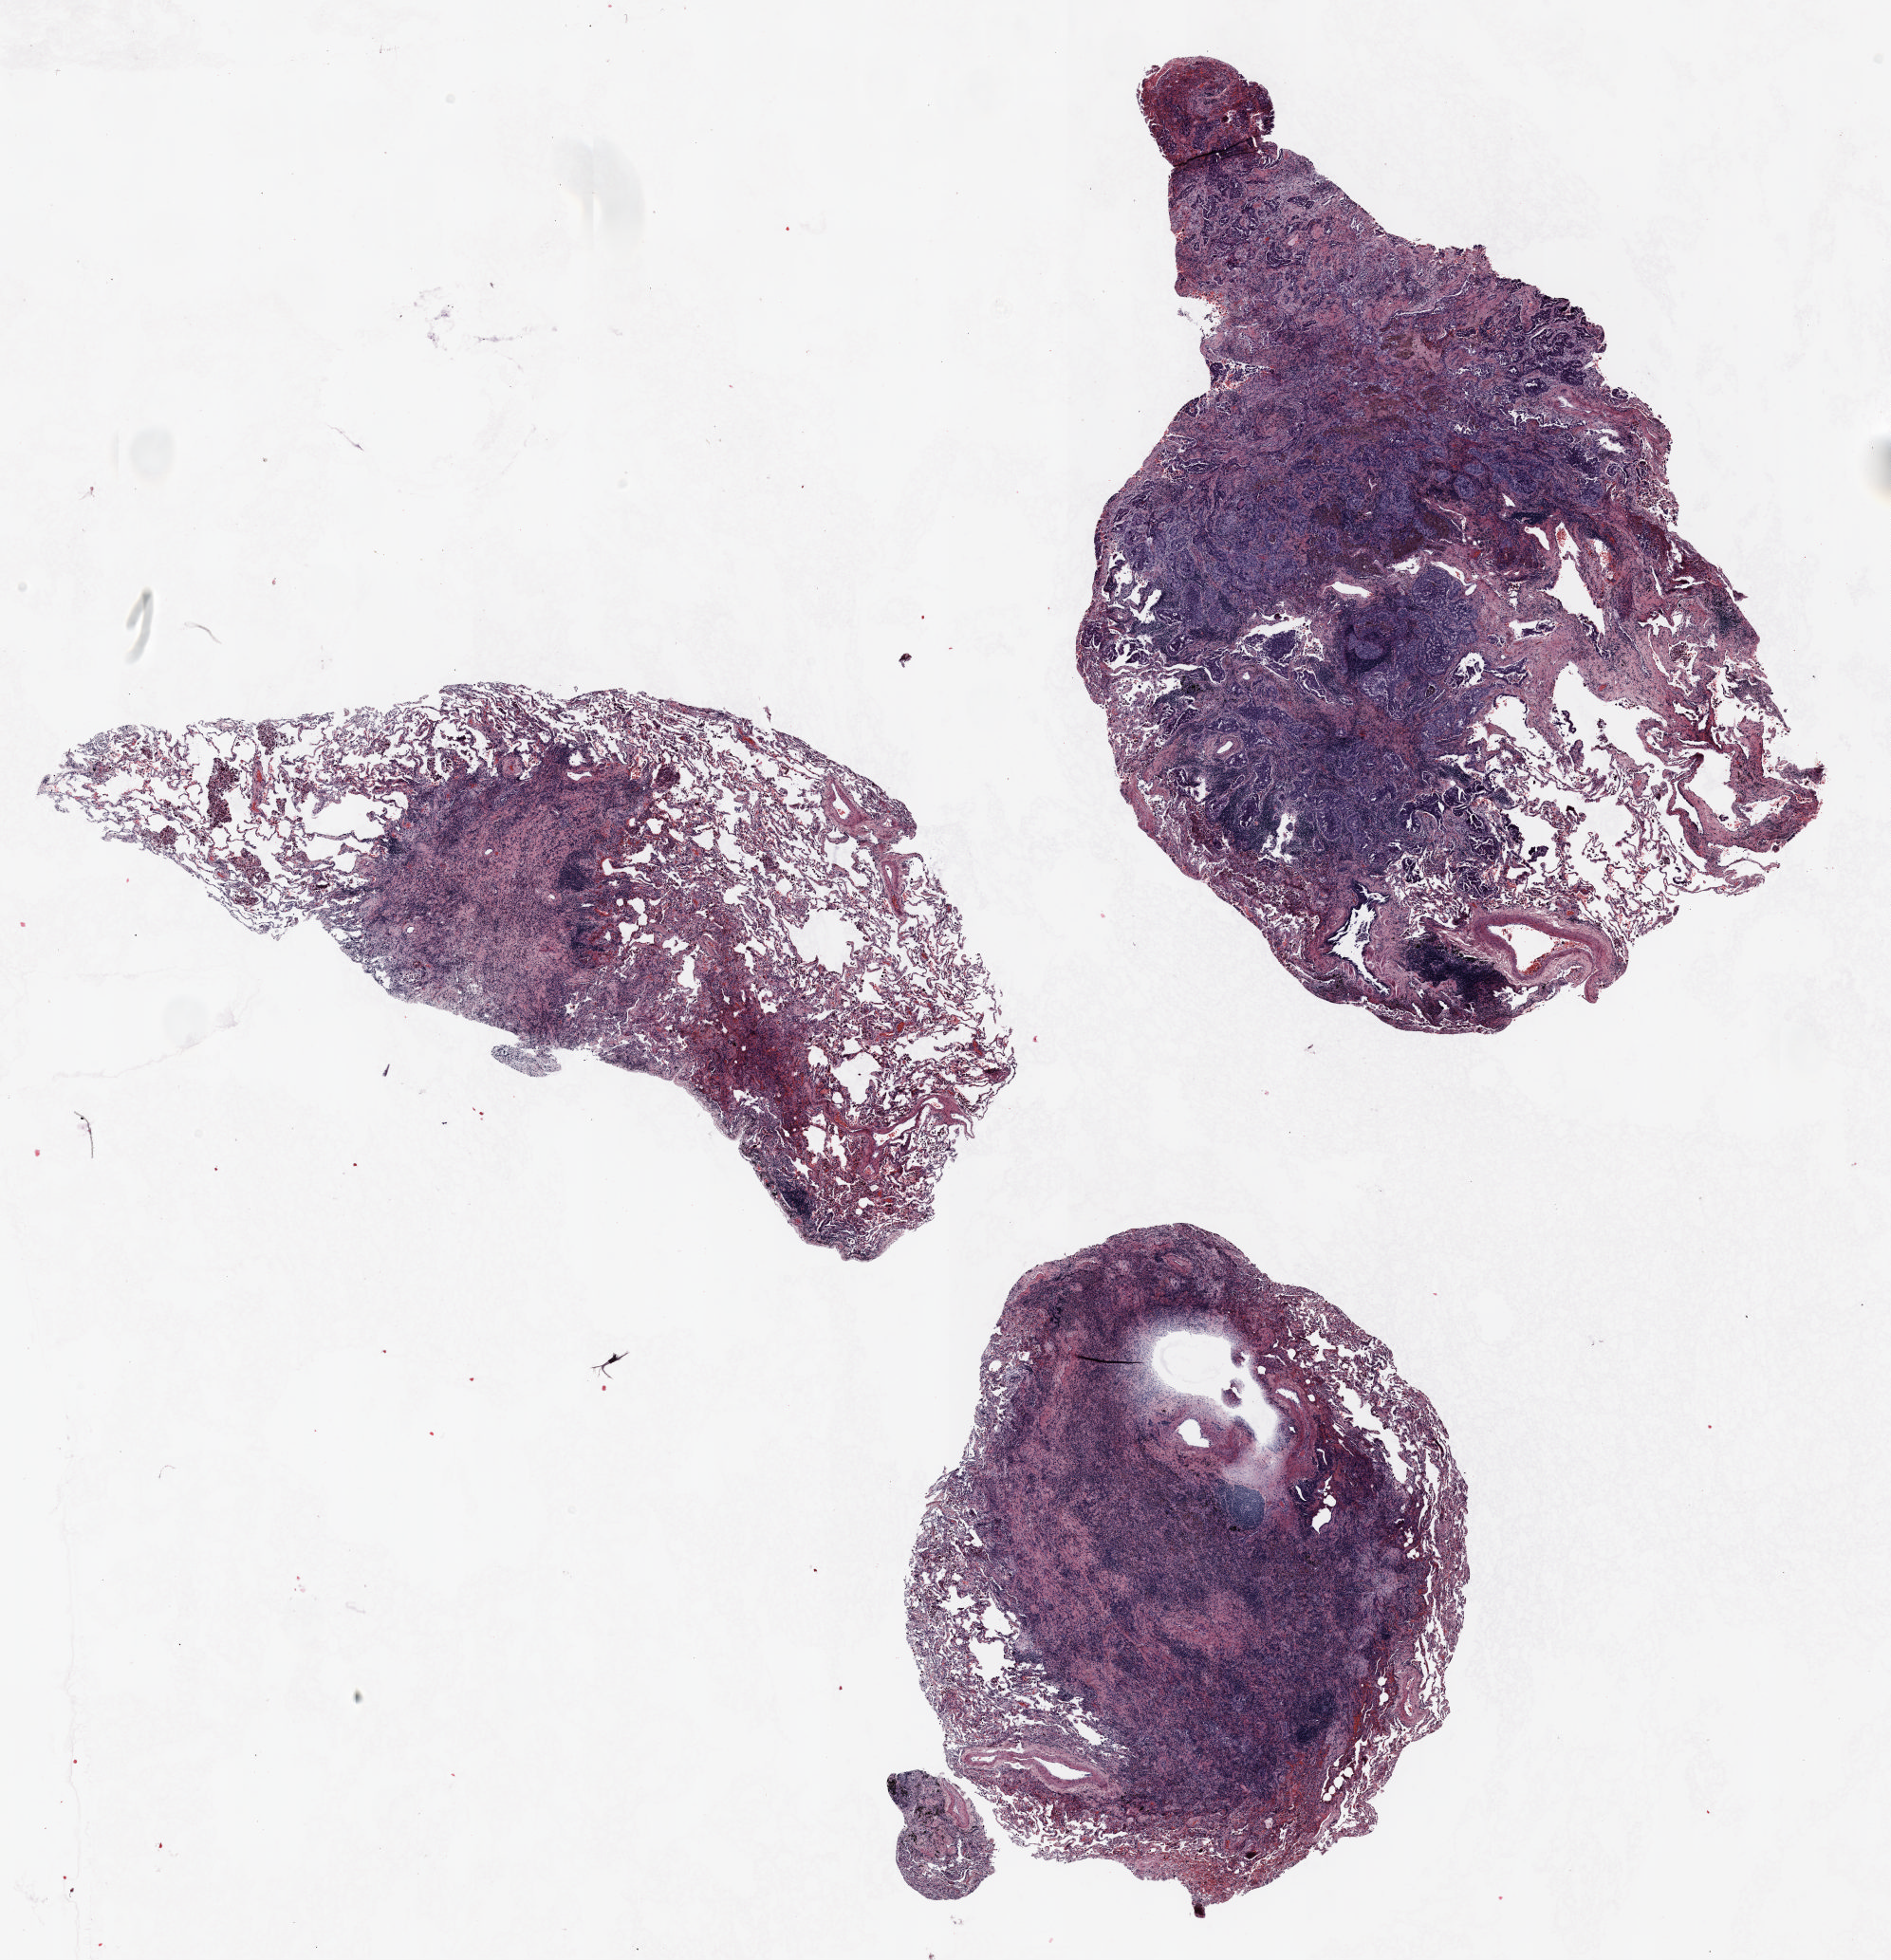
H&E-stained whole-slide image, shown as a low-resolution overview of the whole scanned area (about 16.0 x 16.6 mm, acquisition: 20x scan), FFPE section, lung. Male patient, aged 55 at enrolment. Current smoker at enrolment.
Participant's lung-cancer diagnosis: Adenocarcinoma, NOS.